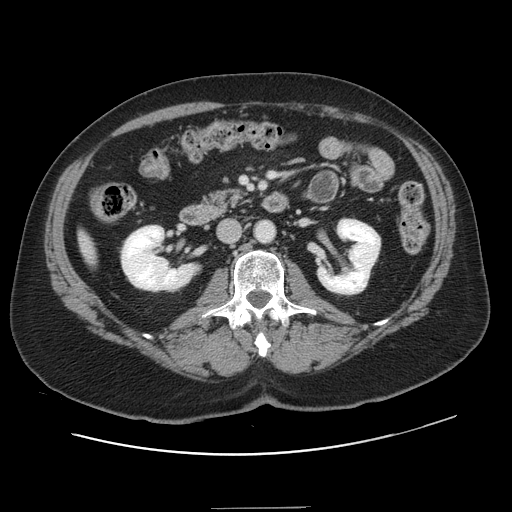
Contrast-enhanced abdominal CT, one axial slice. Position 45 of 143 along the scan axis. 120 kVp. Intravenous contrast given. Soft-tissue window (W 400 / L 40 HU). 2.5 mm slice thickness. 512 × 512 image matrix, field of view 402 × 402 mm. Male patient, age 62 years. From the clinical record (not read from this slice): diagnosis: colorectal cancer liver metastases, imaged before liver resection; multiple liver metastases: yes; largest metastasis: 2.7 cm; disease in both lobes: no.
Outlined on this slice (manually delineated by an expert):
- liver: box from (x=81, y=235) to (x=95, y=260) px